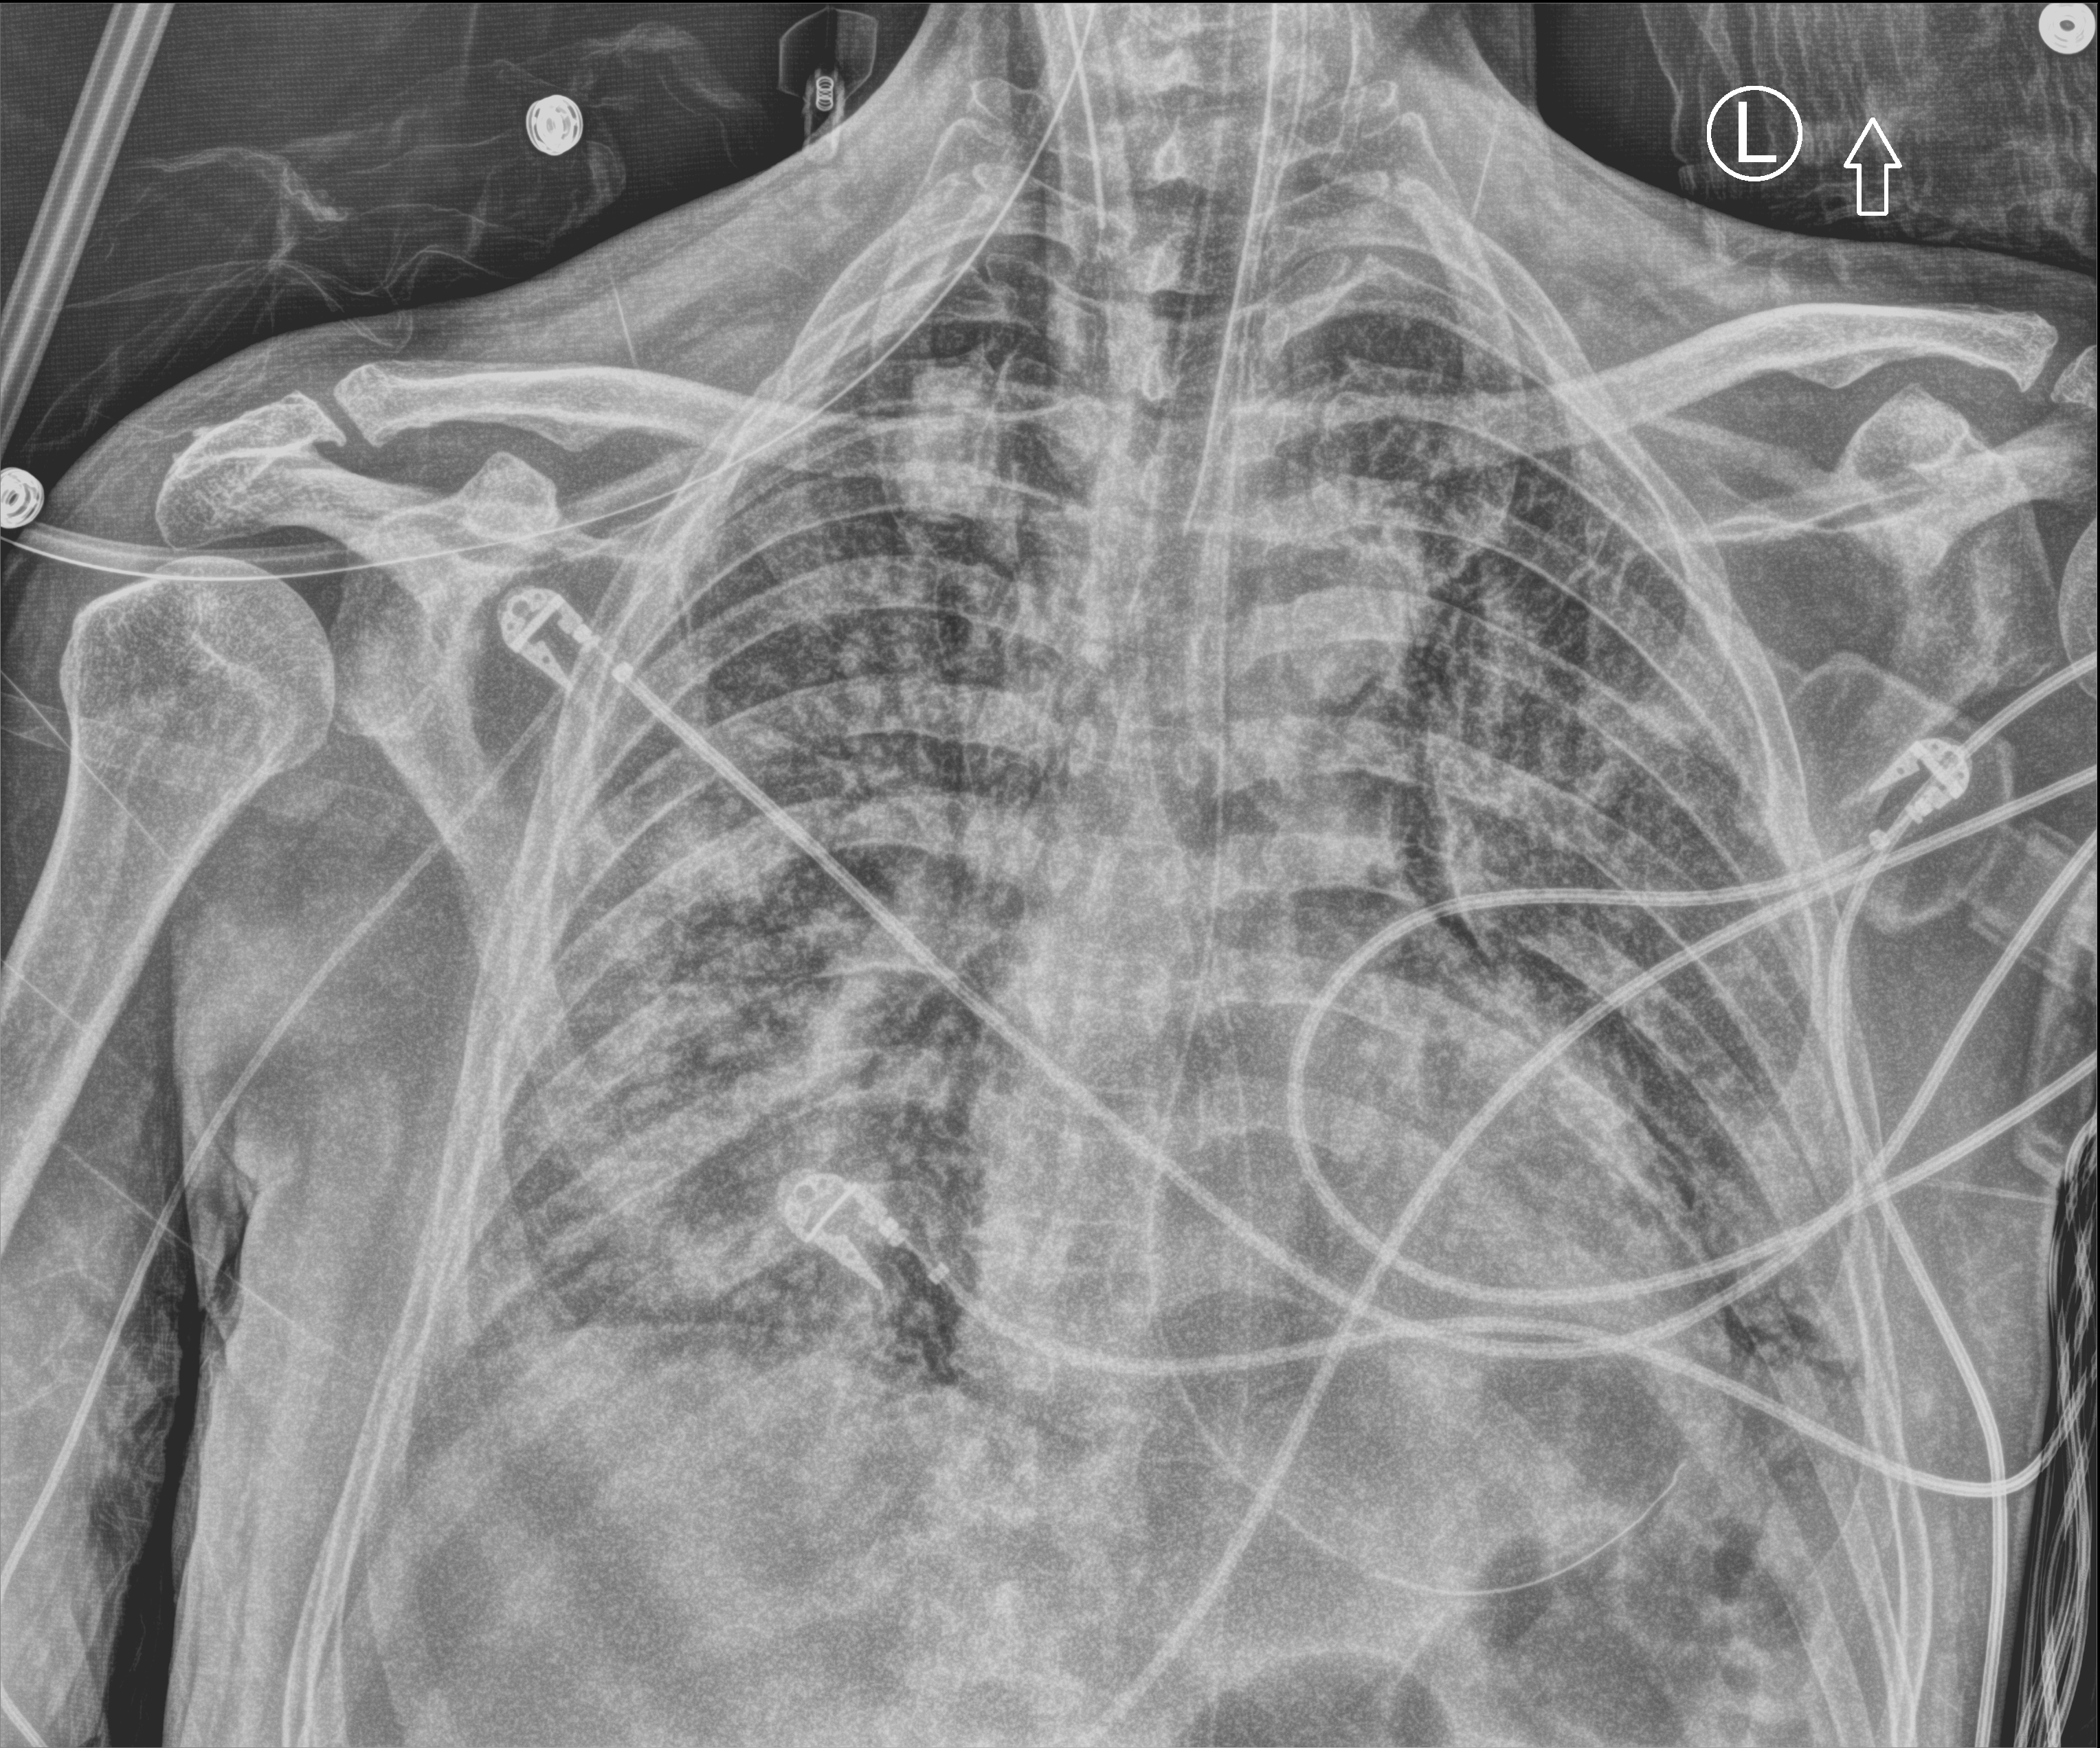
Bedside chest radiograph (computed radiography), anteroposterior (AP) projection. Patient hospitalised with COVID-19; male, aged 60–74 years.
Hospital-stay facts (about this admission, not read from this image; timing relative to this image not recorded):
- admitted to intensive care during this hospital stay: yes